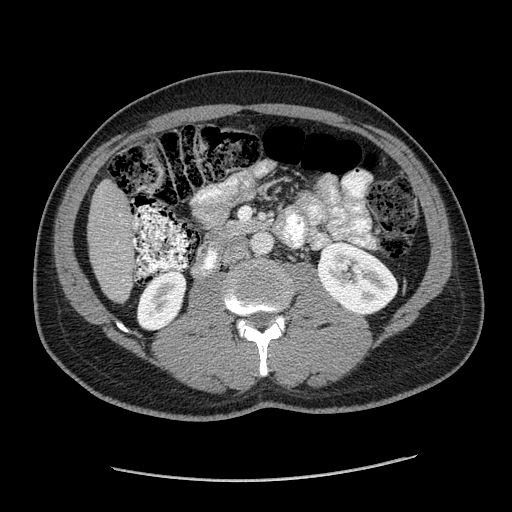
Contrast-enhanced abdominal CT (liver protocol), one axial slice; slice 43 of 182 in the series (ordered by position); reconstruction kernel STANDARD; 120 kVp; soft-tissue window (W 400 / L 40 HU); 2.5 mm slice thickness; 512 × 512 image matrix, field of view 400 × 400 mm. Case-level facts recorded for this patient, not image findings: diagnosis: hepatocellular carcinoma (patient treated with transarterial chemoembolisation; whether this scan precedes or follows treatment is not stated here); TNM stage (as recorded): Stage-I; Child-Pugh class: A; tumour differentiation: well differentiated; tumour nodularity: uninodular.
Annotated regions visible in this slice (semi-automatically segmented with operator editing):
- liver parenchyma outside the tumour (the mass and vessels are separate outlines, so this box may not span the whole liver): box from (x=88, y=179) to (x=136, y=302) px
- liver vessels: (x=133, y=239)–(x=136, y=243)